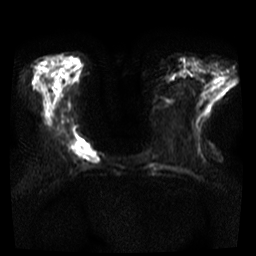
Breast MRI, one axial slice. Position 11 of 35 along the scan axis. Diffusion-weighted series; image 2 of 4 stored at this slice position (different b-values; order by instance number). 3 T. 256 × 256 image matrix, field of view 300 × 300 mm. Female patient.
Outlined on this slice (expert manual segmentation):
- tumour on diffusion-weighted imaging: bounding box (x1, y1, x2, y2) in pixels: (72, 139, 99, 164)